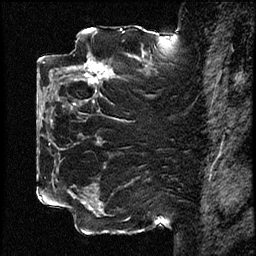
Breast MRI (dynamic contrast-enhanced), one sagittal slice; position 40 of 78 along the scan axis; dynamic contrast-enhanced study with each time point stored as its own series, time point 2 of 3 at this slice position (early post-contrast, ordered by acquisition time); 1.5 T; TE 4.2 ms, TR 17.6 ms; 2 mm slice thickness; 256 × 256 image matrix, field of view 200 × 200 mm. Female patient, age 42 years. From the clinical record (not read from this slice): setting: breast cancer imaged before/during neoadjuvant chemotherapy; receptor status: HER2-positive.
Annotated regions visible in this slice (semi-automatically segmented with operator editing):
- analysis volume of interest (the breast-tissue region the enhancement analysis was run in; not a lesion): bounding box (x1, y1, x2, y2) in pixels: (50, 48, 131, 128)
- tumour enhancement mask (voxels above the 100 % enhancement threshold inside the analysis volume of interest): (84, 60, 113, 84)